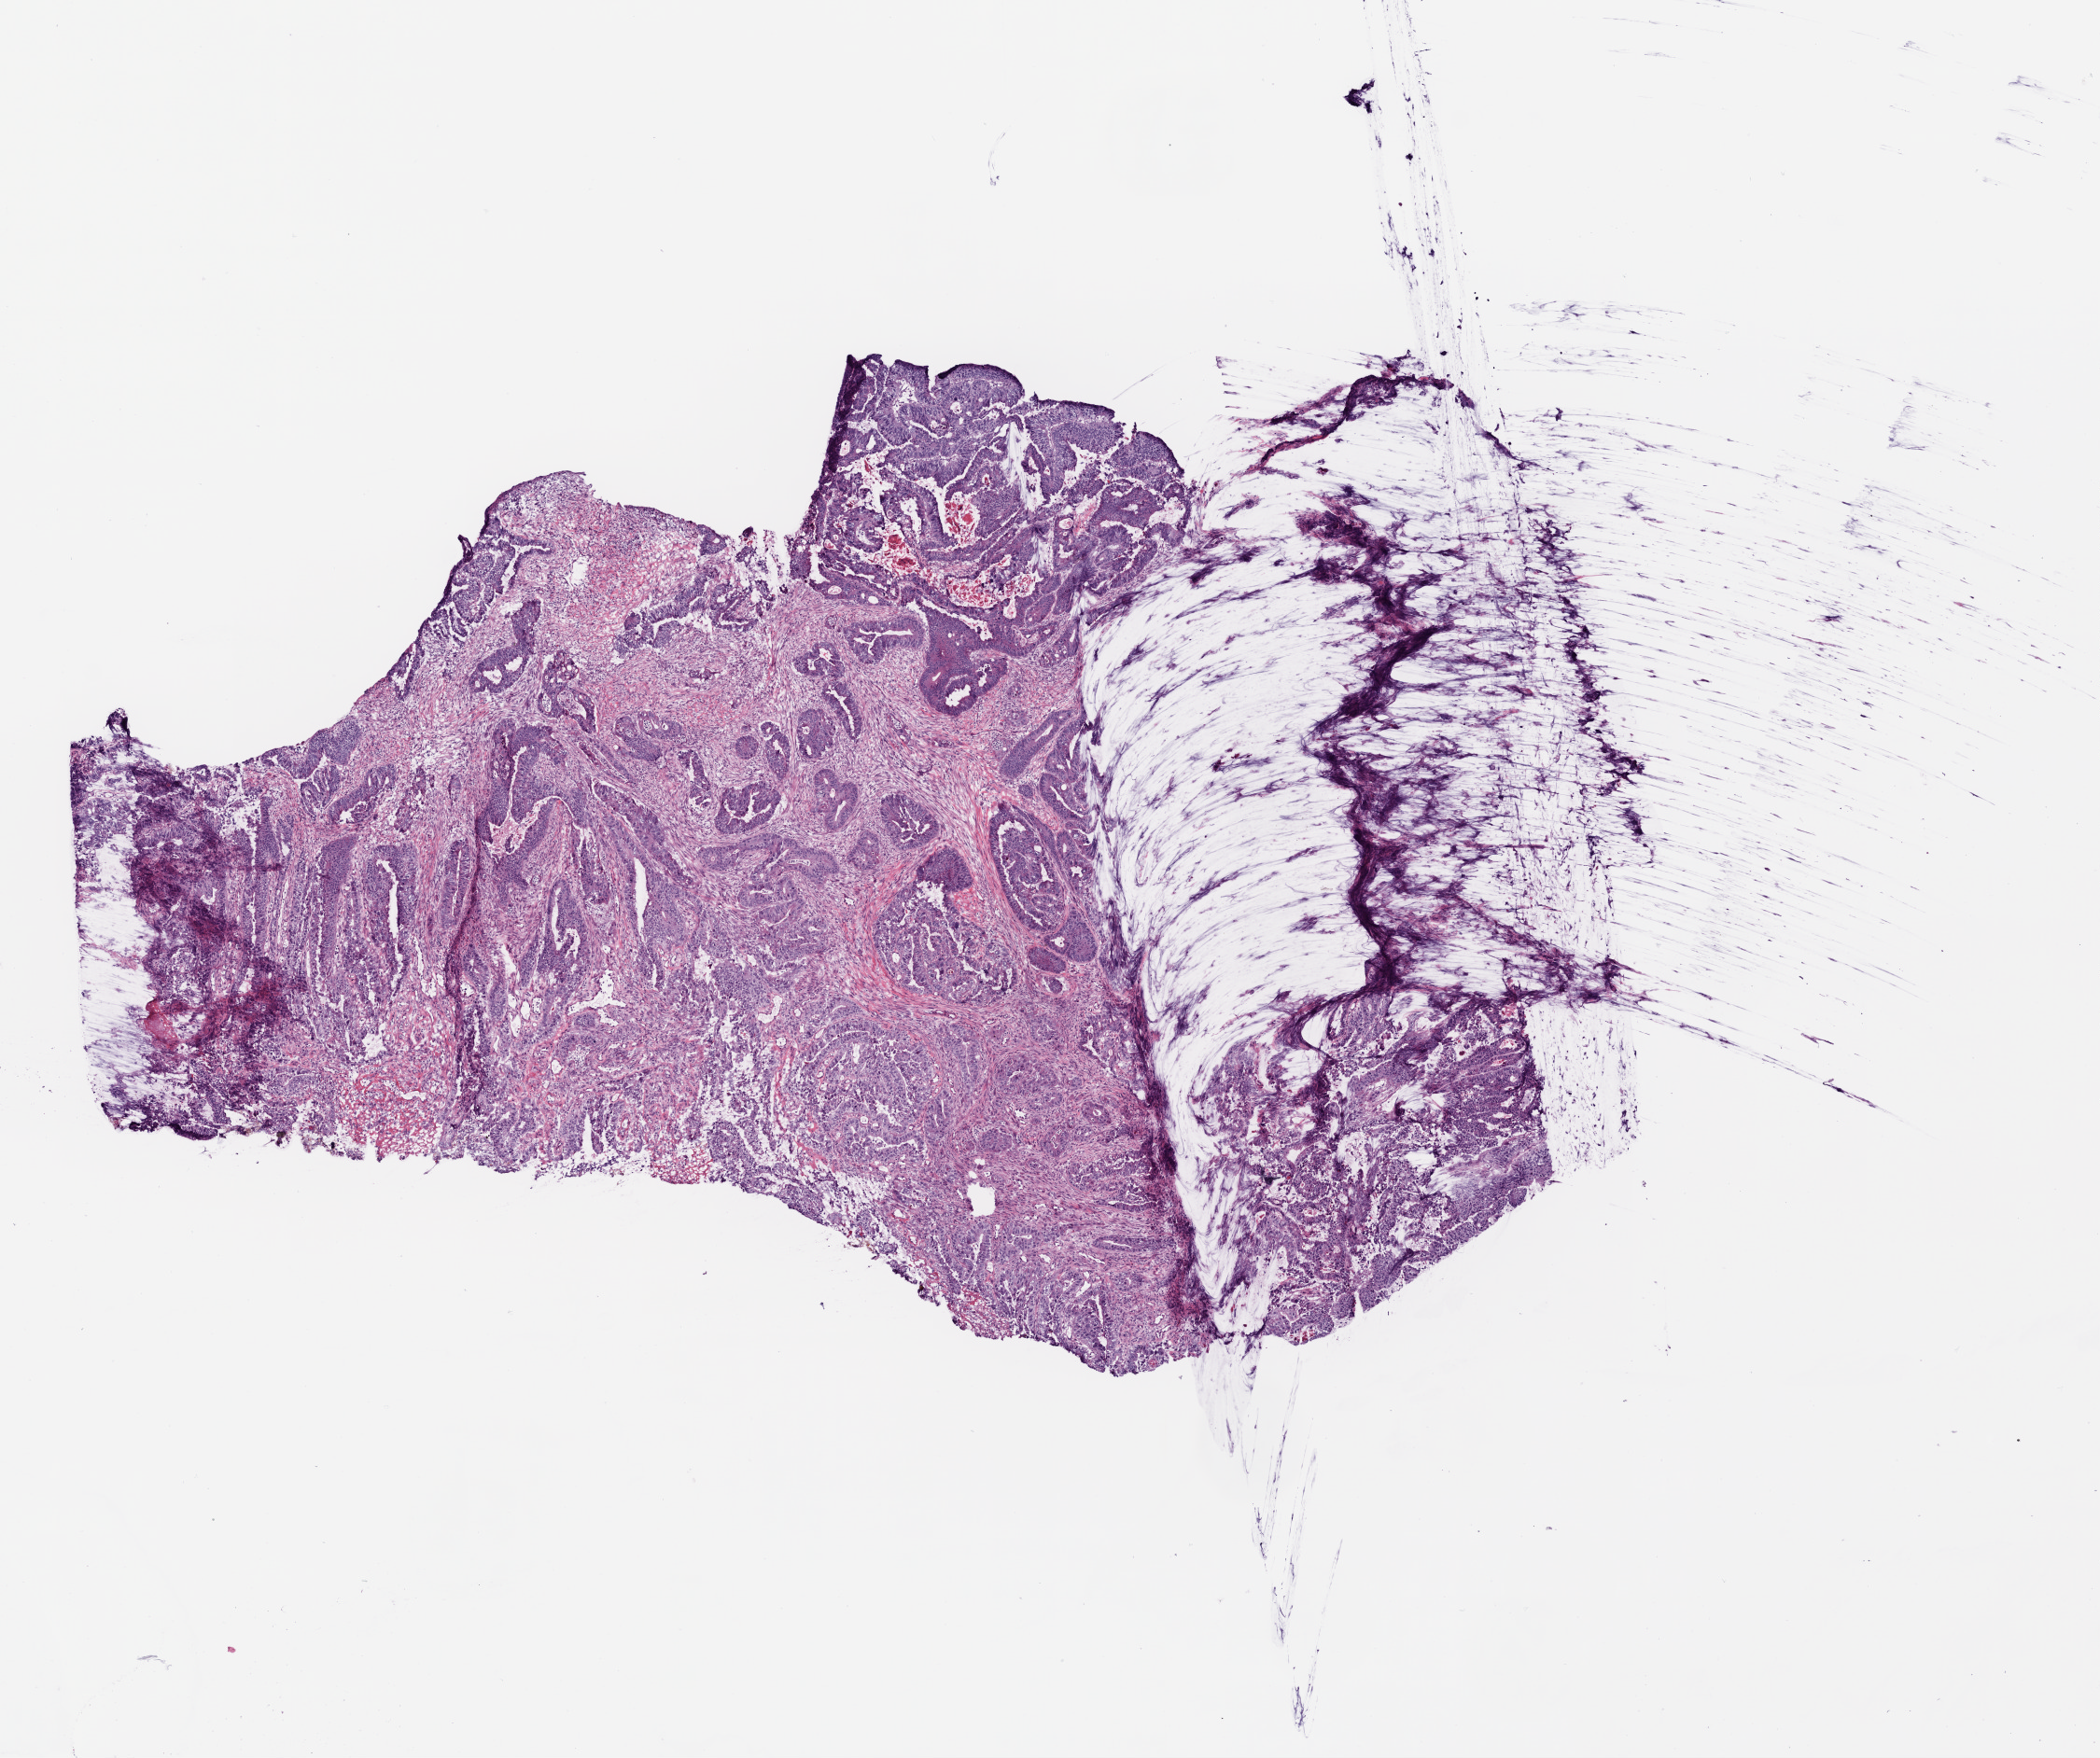
Digitized Hematoxylin and eosin (H&E) stained tissue section (whole slide), shown as a low-resolution overview of the whole scanned area (about 9.0 x 7.6 mm, acquisition: 20x scan). Frozen section from the top of the tissue portion. Colon, primary tumour sample. Male patient; age at initial diagnosis 72 years. Composition of this section per pathologist review: tumour cells 70%, tumour nuclei 90%, normal cells 0%, stromal cells 30%, necrosis 0%.
• lymph nodes positive (case pathology): 3 of 12 examined
• histologic diagnosis: Adenocarcinoma, NOS (sigmoid colon)
• AJCC pathologic stage: IV